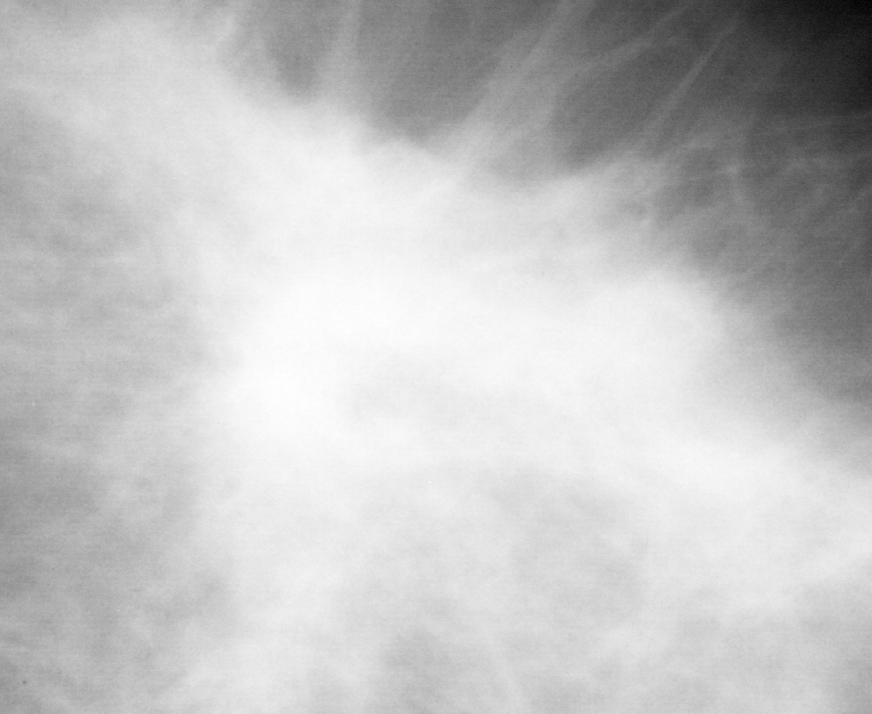
Crop from a digitized film mammogram around one marked abnormality, left breast, MLO view.
Marked abnormality: mass, shape irregular, margins spiculated; BI-RADS assessment category 5; pathology (as recorded): malignant.